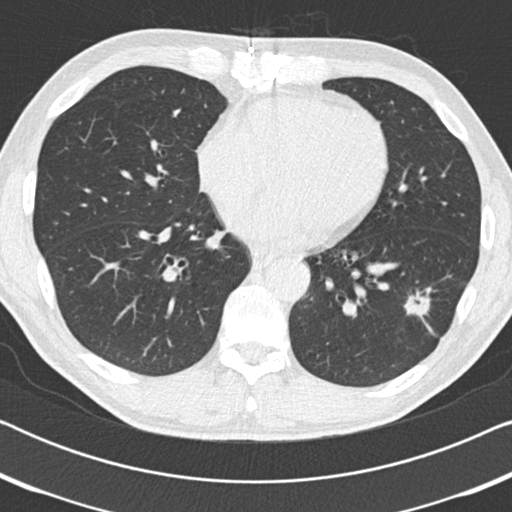
Low-dose screening chest CT, axial slice; third screening round (two years after baseline); lung window (W 1500 / L -600 HU); 2 mm slice thickness; 512 × 512 image matrix, field of view 330 × 330 mm. Male participant, aged 59 years at enrolment.
- Expert reader's lesion annotation, bounding box <389,277,456,340> (left, top, right, bottom; pixels).
- The screening reader recorded 2 non-calcified nodules or masses ≥4 mm on this exam (left lower lobe, right middle lobe); which of them this box marks is not recorded.
- Lung cancer was diagnosed 73 days after this screen: adenocarcinoma, NOS, left lower lobe, poorly differentiated (G3), stage IA (AJCC 6th edition), 20 mm at pathology.